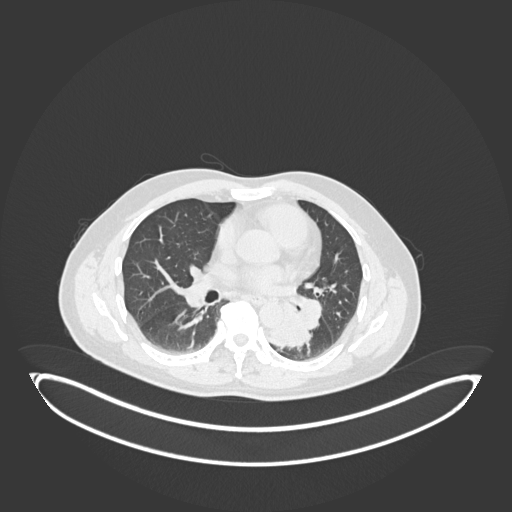
Chest CT, one axial slice; slice 100 of 258 in the series (ordered by position); lung window (W 1500 / L -600 HU); 1 mm slice thickness; 512 × 512 image matrix, field of view 500 × 500 mm. Patient: male, 54 years. From the clinical record (not read from this slice): clinical TNM (as recorded): T3 N0 M0.
Annotated regions visible in this slice (bounding box drawn by a radiologist):
- lung tumour (recorded histology: squamous cell carcinoma): box from (x=272, y=306) to (x=314, y=352) px